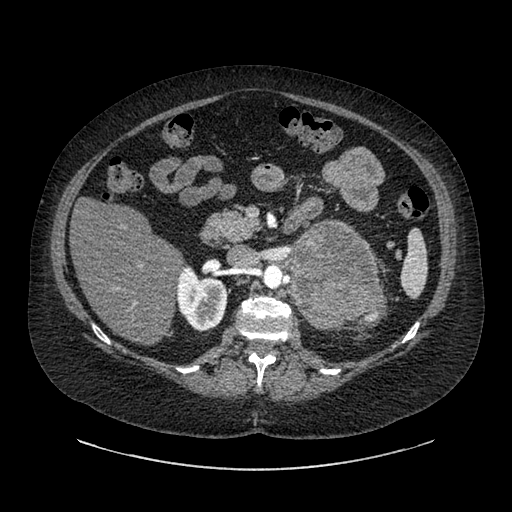
Contrast-enhanced abdominal CT, one axial slice; slice 538 of 769 in the series (ordered by position); intravenous contrast given; soft-tissue window (W 400 / L 40 HU); 0.62 mm slice thickness; 512 × 512 image matrix. Patient: female, 61 years. Case-level facts recorded for this patient, not image findings: diagnosis: adrenocortical carcinoma; tumour side: left adrenal; tumour size at pathology: 13 cm; Ki-67 index: 79 %; stage (as recorded): 2.
Outlined on this slice (semi-automatically segmented with operator editing):
- mass: bounding box <291,224,375,328> (left, top, right, bottom; pixels)